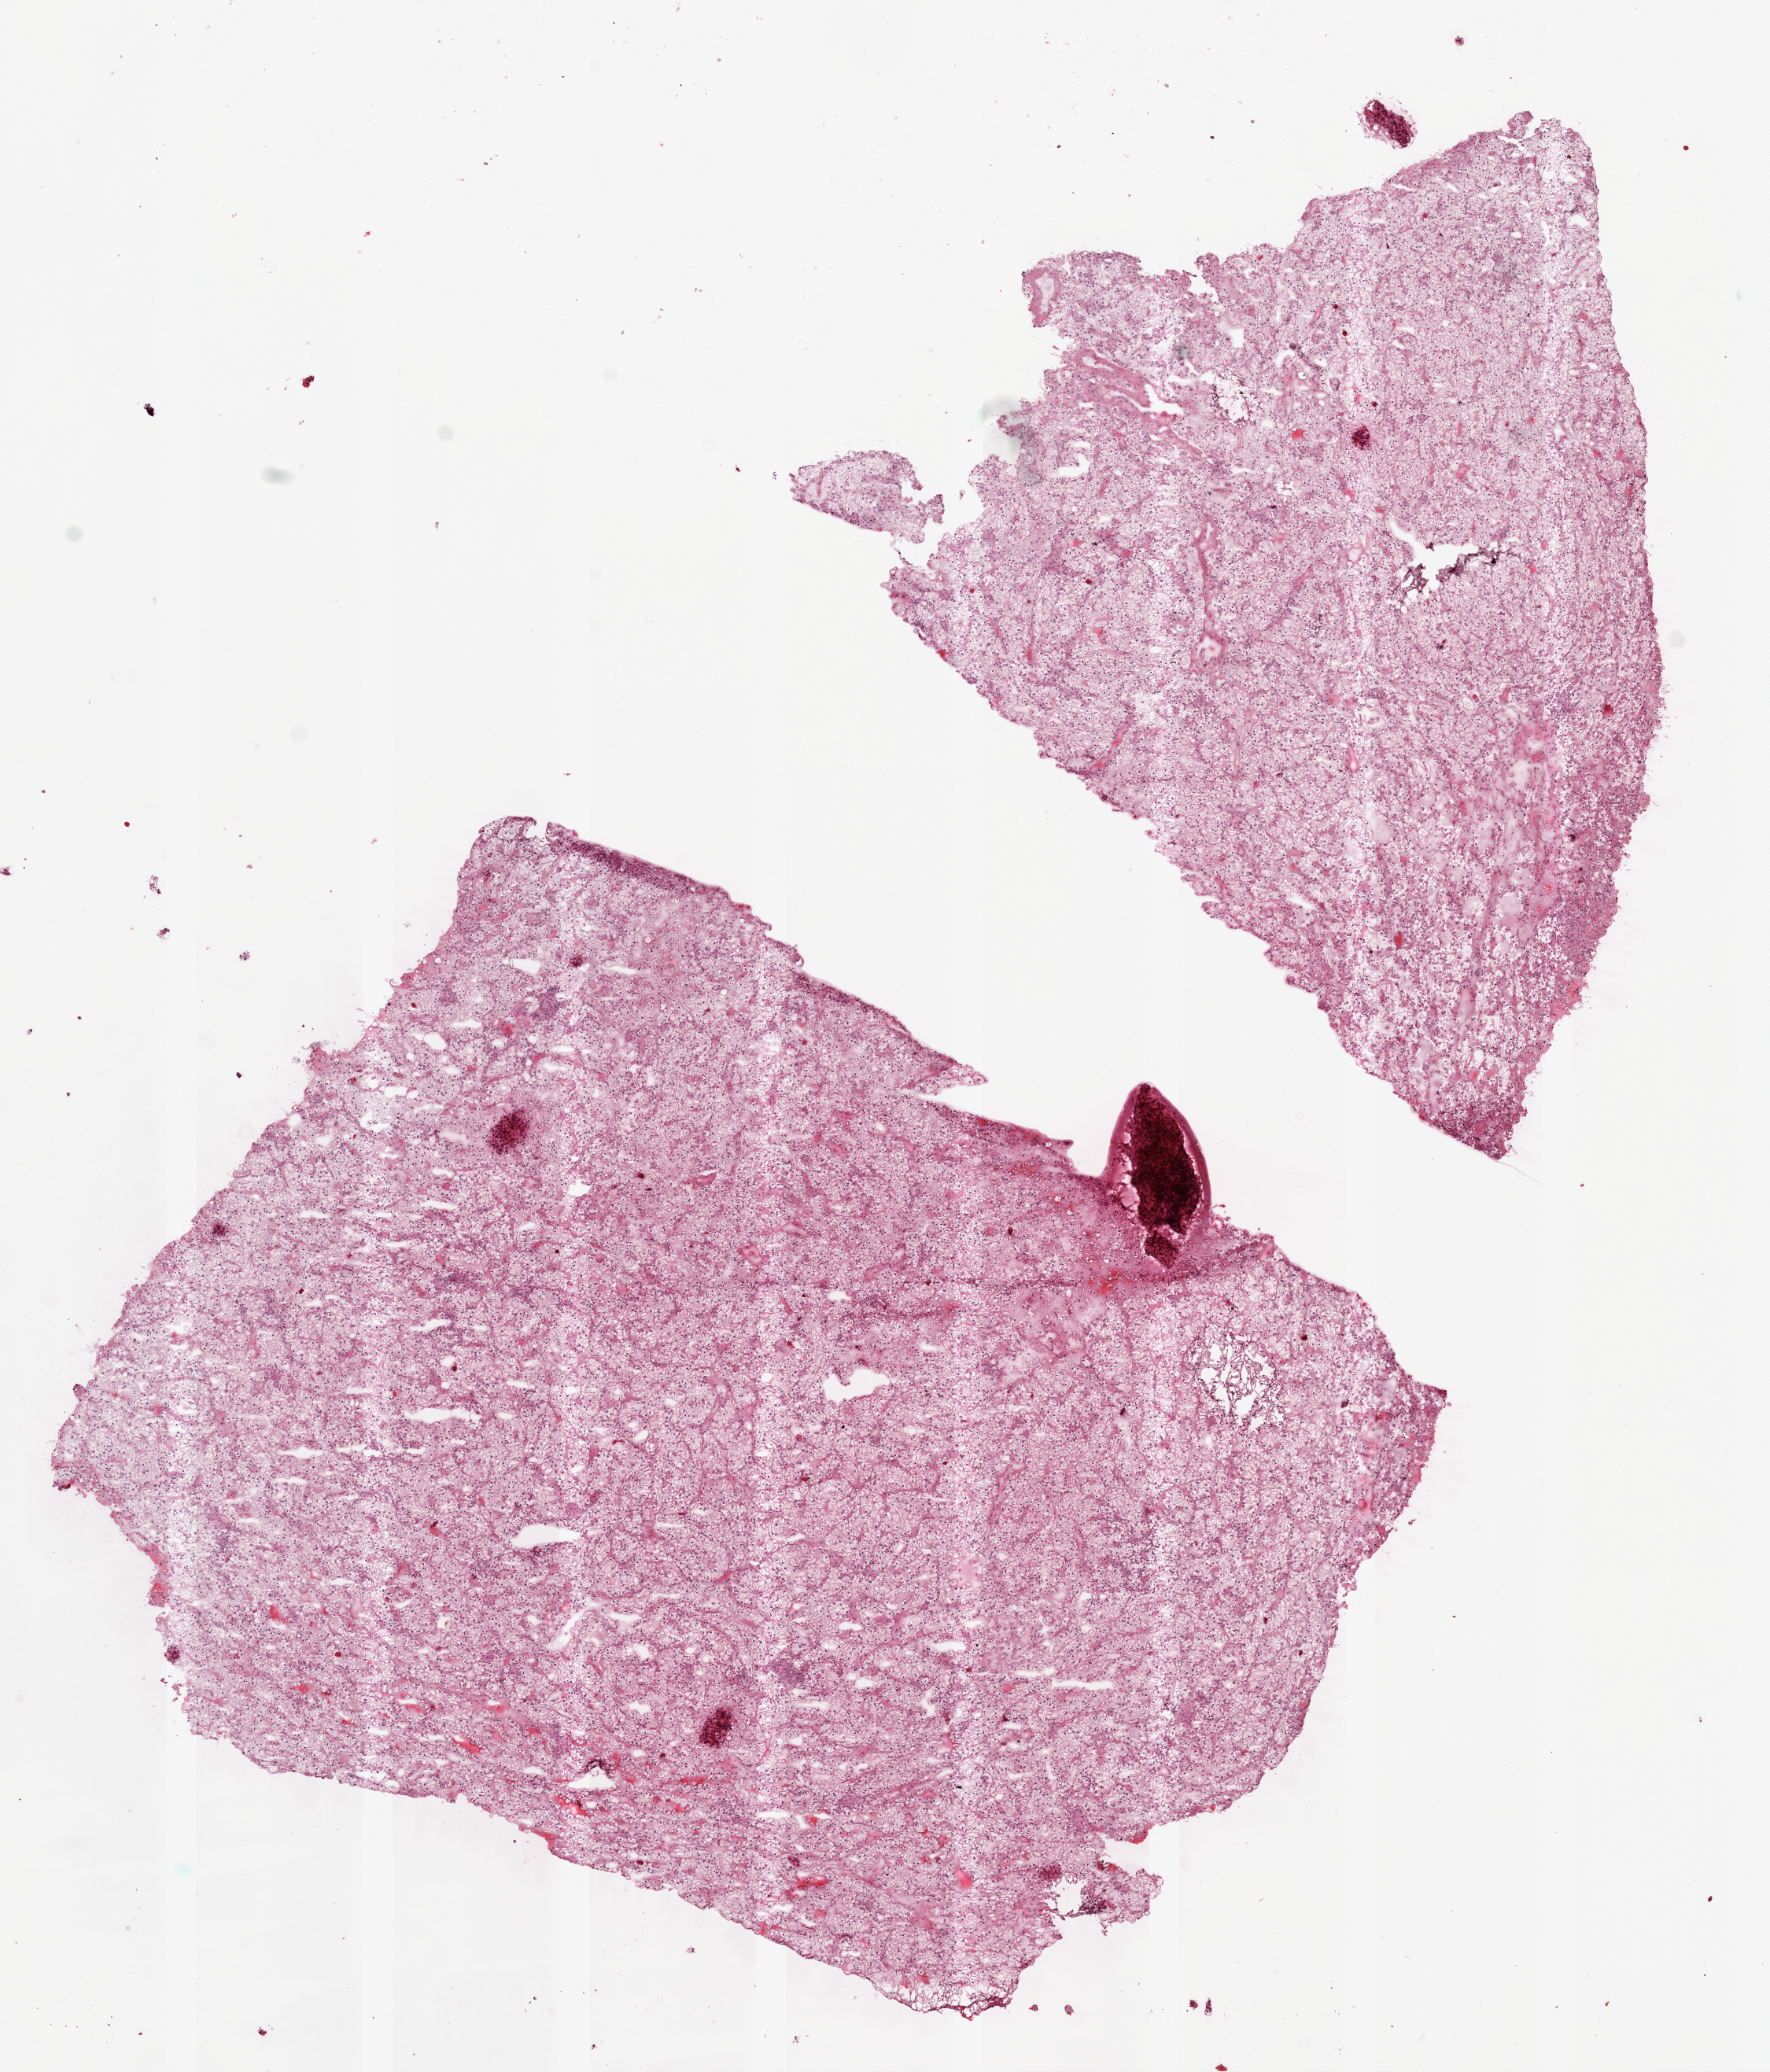
H&E whole-slide image — low-resolution overview of the scanned area, about 9.0 x 10.6 mm. Frozen section. Primary tumour sample from the kidney. Male, age 79 years at initial diagnosis. Histologic grade: G2 (moderately differentiated). Pathologist review of this section (percent, as recorded): tumour cells 95%, tumour nuclei 90%, normal cells 0%, stromal cells 5%, necrosis 0%.
- histologic diagnosis: Clear cell adenocarcinoma, NOS
- laterality: left
- lymph nodes positive (case pathology): 0 of 1 examined
- AJCC pathologic stage: III